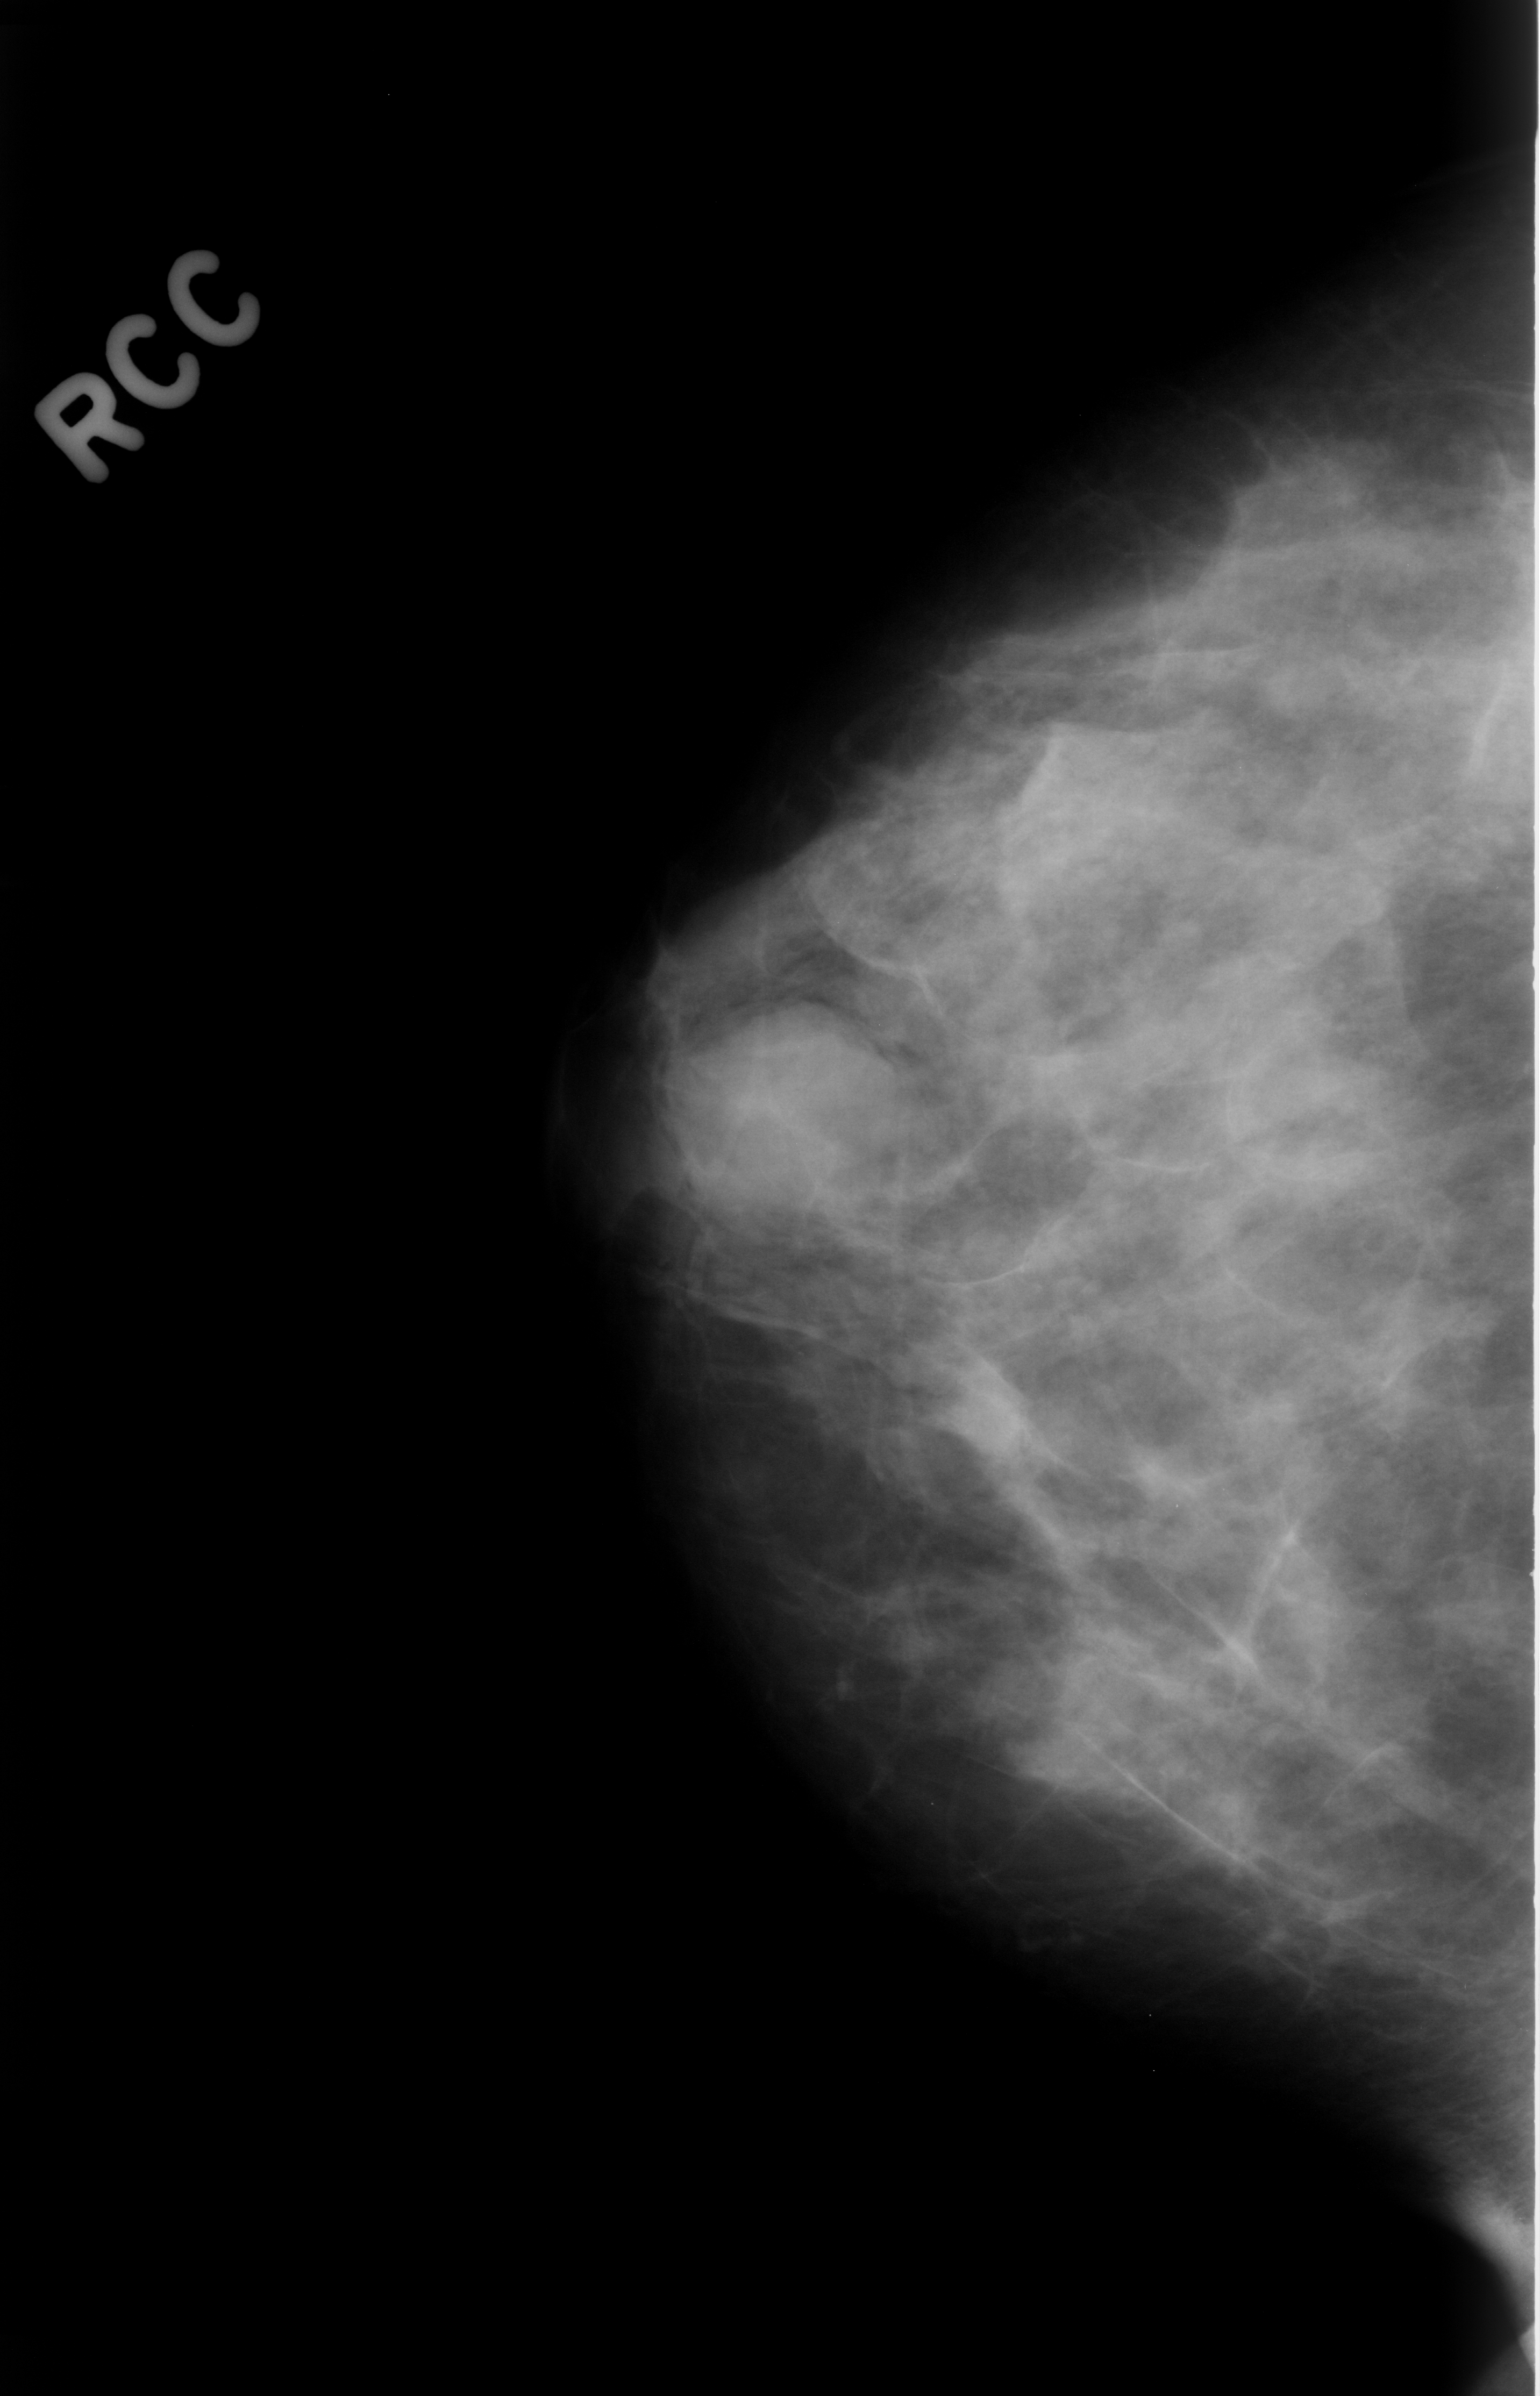
Digitized screen-film mammogram; right breast; CC view; breast composition: scattered fibroglandular densities (BI-RADS density category 2 of 4); 1540 × 2396 image matrix.
Expert-marked regions of interest on this image (one box per marked abnormality):
- mass, shape oval, margins circumscribed; BI-RADS assessment category 4; subtlety rating 4 on a 1 (subtle) to 5 (obvious) scale; pathology (as recorded): benign: bounding box [x1, y1, x2, y2] px = [675, 1001, 897, 1231]